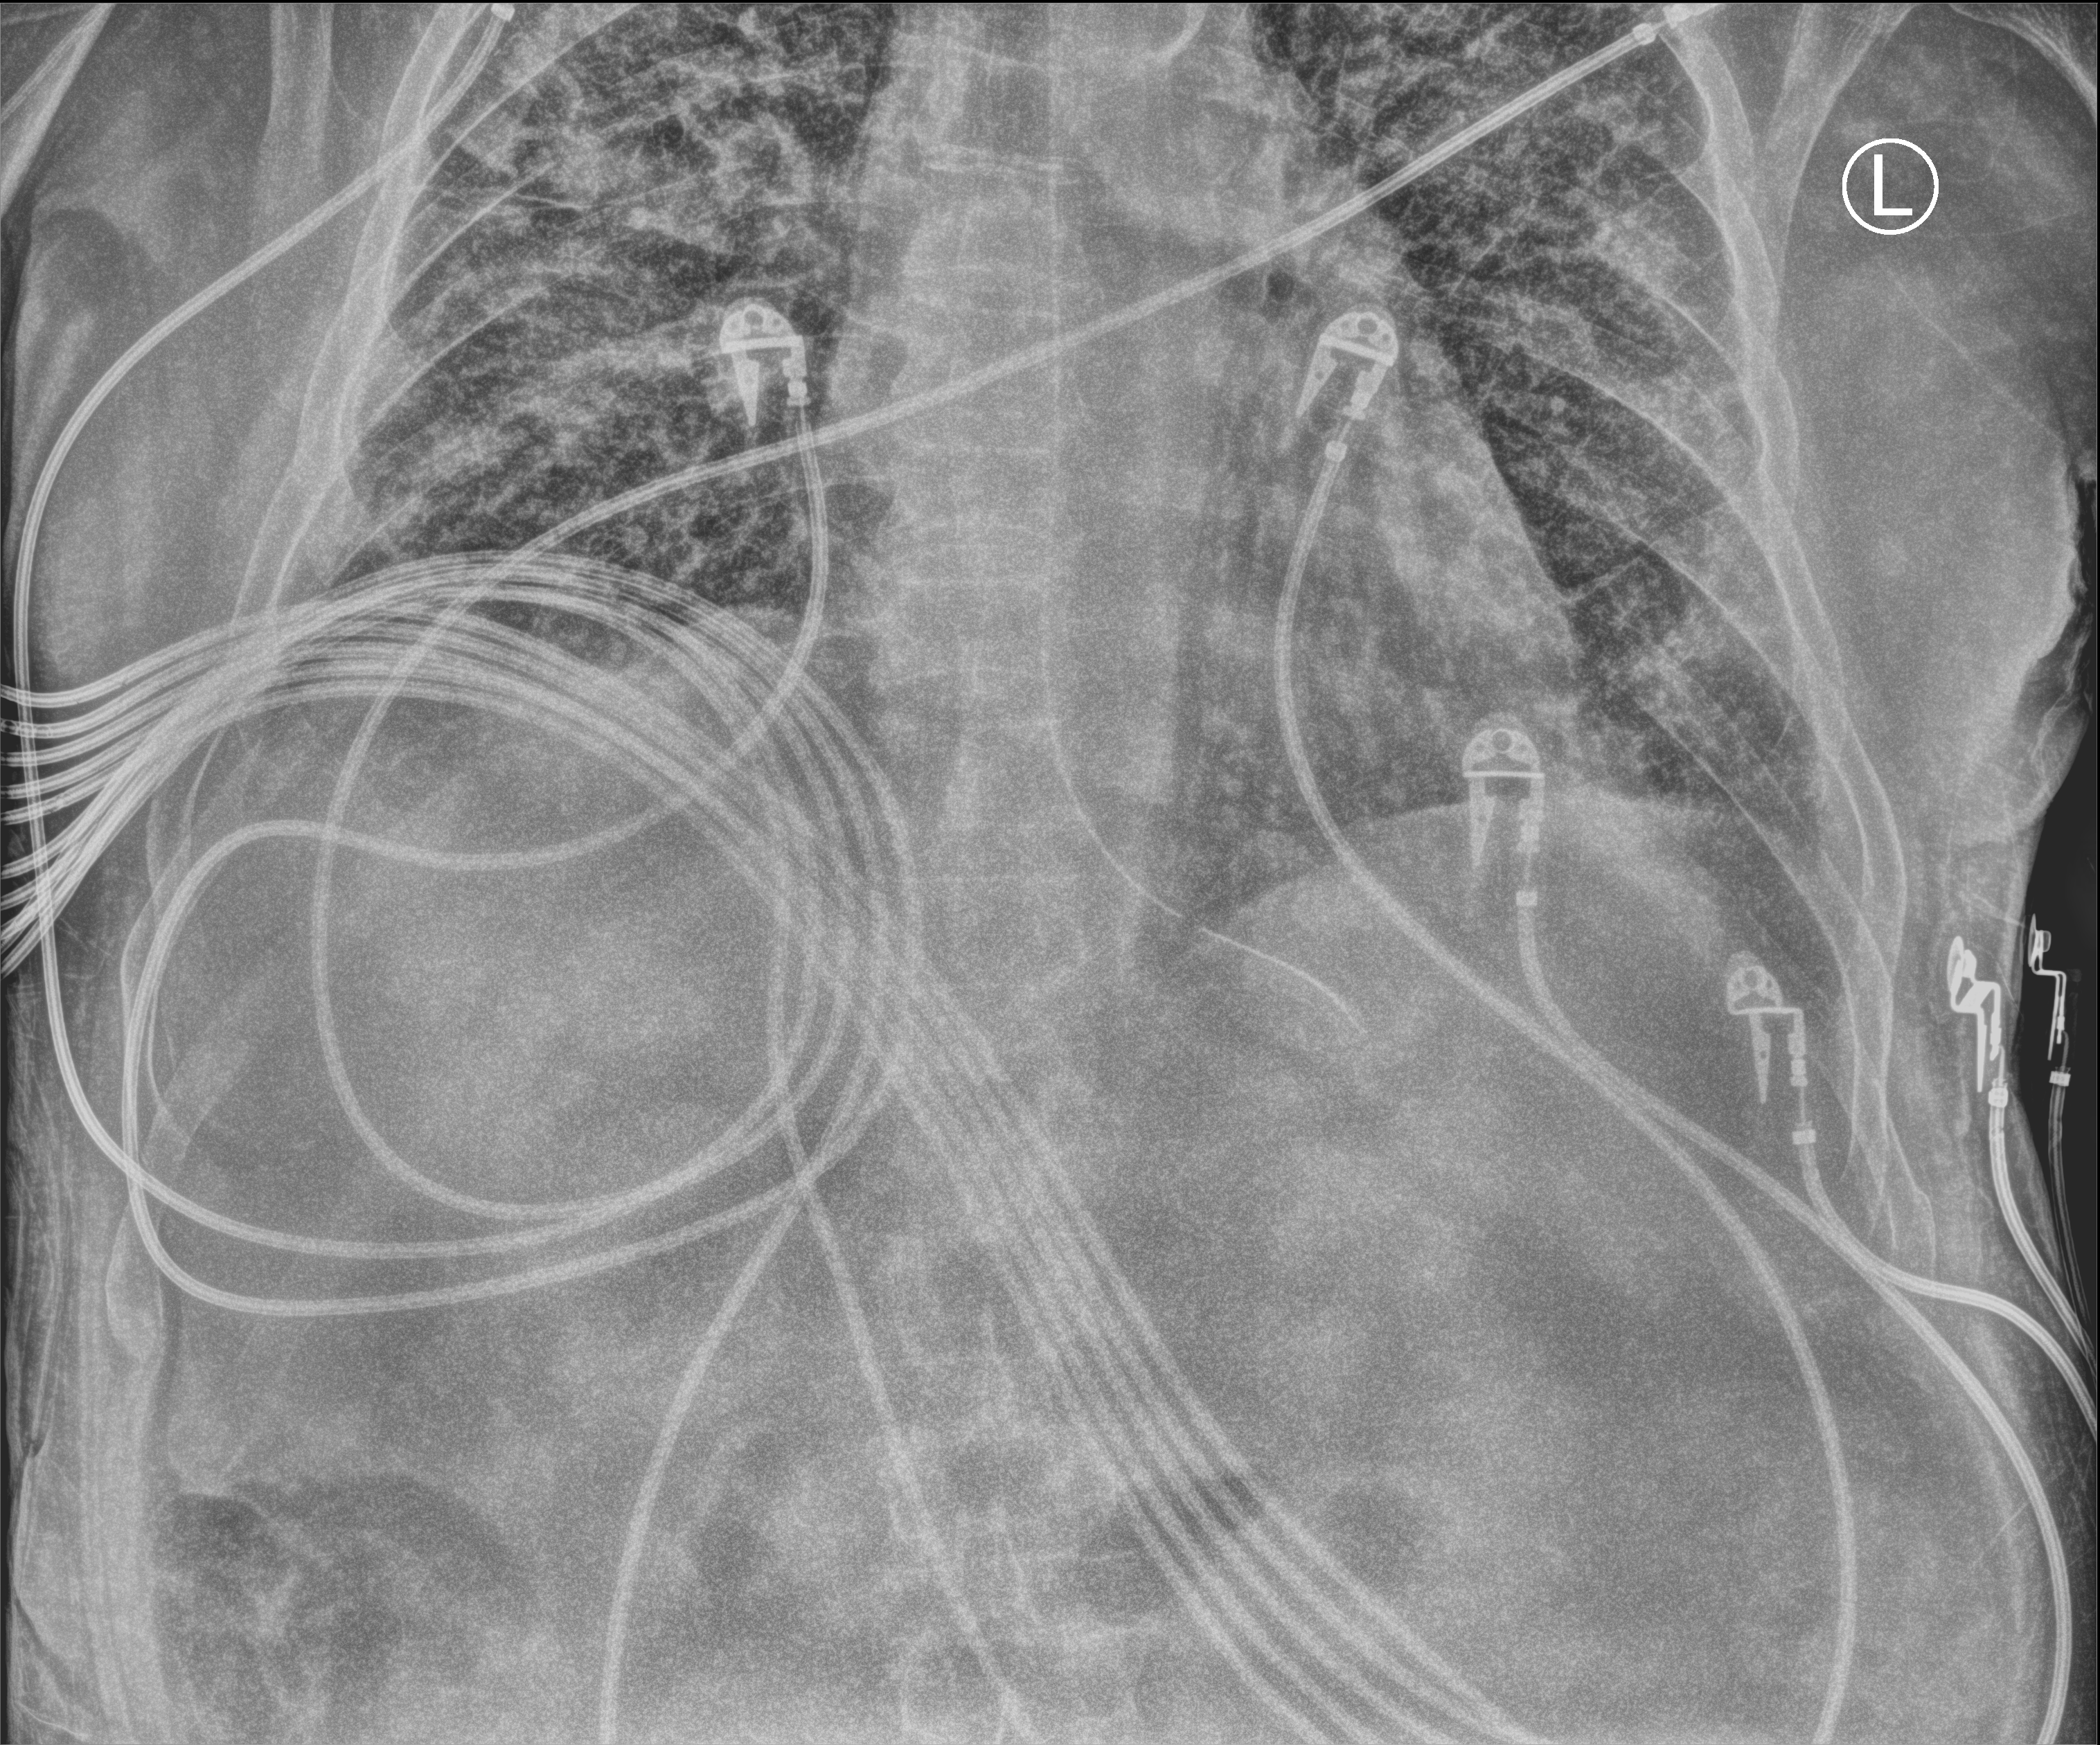
Bedside chest radiograph (computed radiography); anteroposterior (AP) projection. Male patient hospitalised with COVID-19, age 60–74 years.
Hospital-stay facts (about this admission, not read from this image; timing relative to this image not recorded): admitted to intensive care during this hospital stay: yes; mechanically ventilated during this hospital stay: yes.